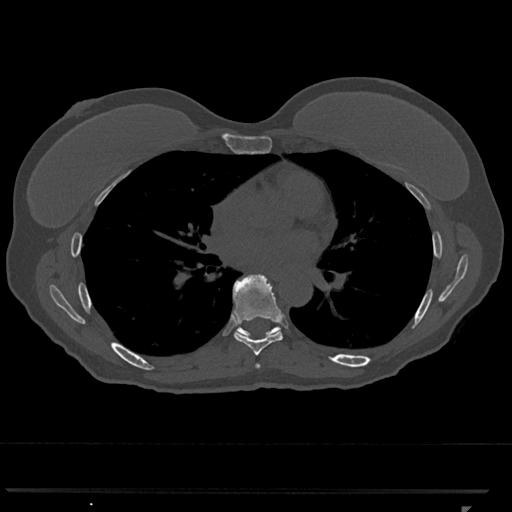
CT including the spine, one axial slice. Slice 702 of 793 in the series (ordered by position). 120 kVp. Bone window (W 1800 / L 400 HU). 0.5 mm slice thickness. 512 × 512 image matrix, field of view 380 × 380 mm. Female patient, age 62 years. Case-level facts recorded for this patient, not image findings: primary cancer: renal.
Annotated regions visible in this slice (semi-automatic segmentation, software-assisted and operator-edited):
- T6 vertebra: box from (x=255, y=363) to (x=261, y=368) px
- T7 vertebra: (x=233, y=274)–(x=283, y=356)
- T8 vertebra: (x=238, y=327)–(x=278, y=335)